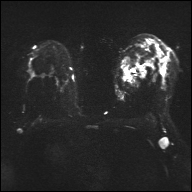
Breast MRI, one axial slice. Slice 25 of 32 in the series (ordered by position). Diffusion-weighted series; image 2 of 4 stored at this slice position (different b-values; order by instance number). 1.5 T. 4 mm slice thickness. 192 × 192 image matrix, field of view 360 × 360 mm. Female patient.
Outlined on this slice (outlined manually by an expert reader):
- tumour on diffusion-weighted imaging: bounding box (x1, y1, x2, y2) in pixels: (140, 71, 144, 77)